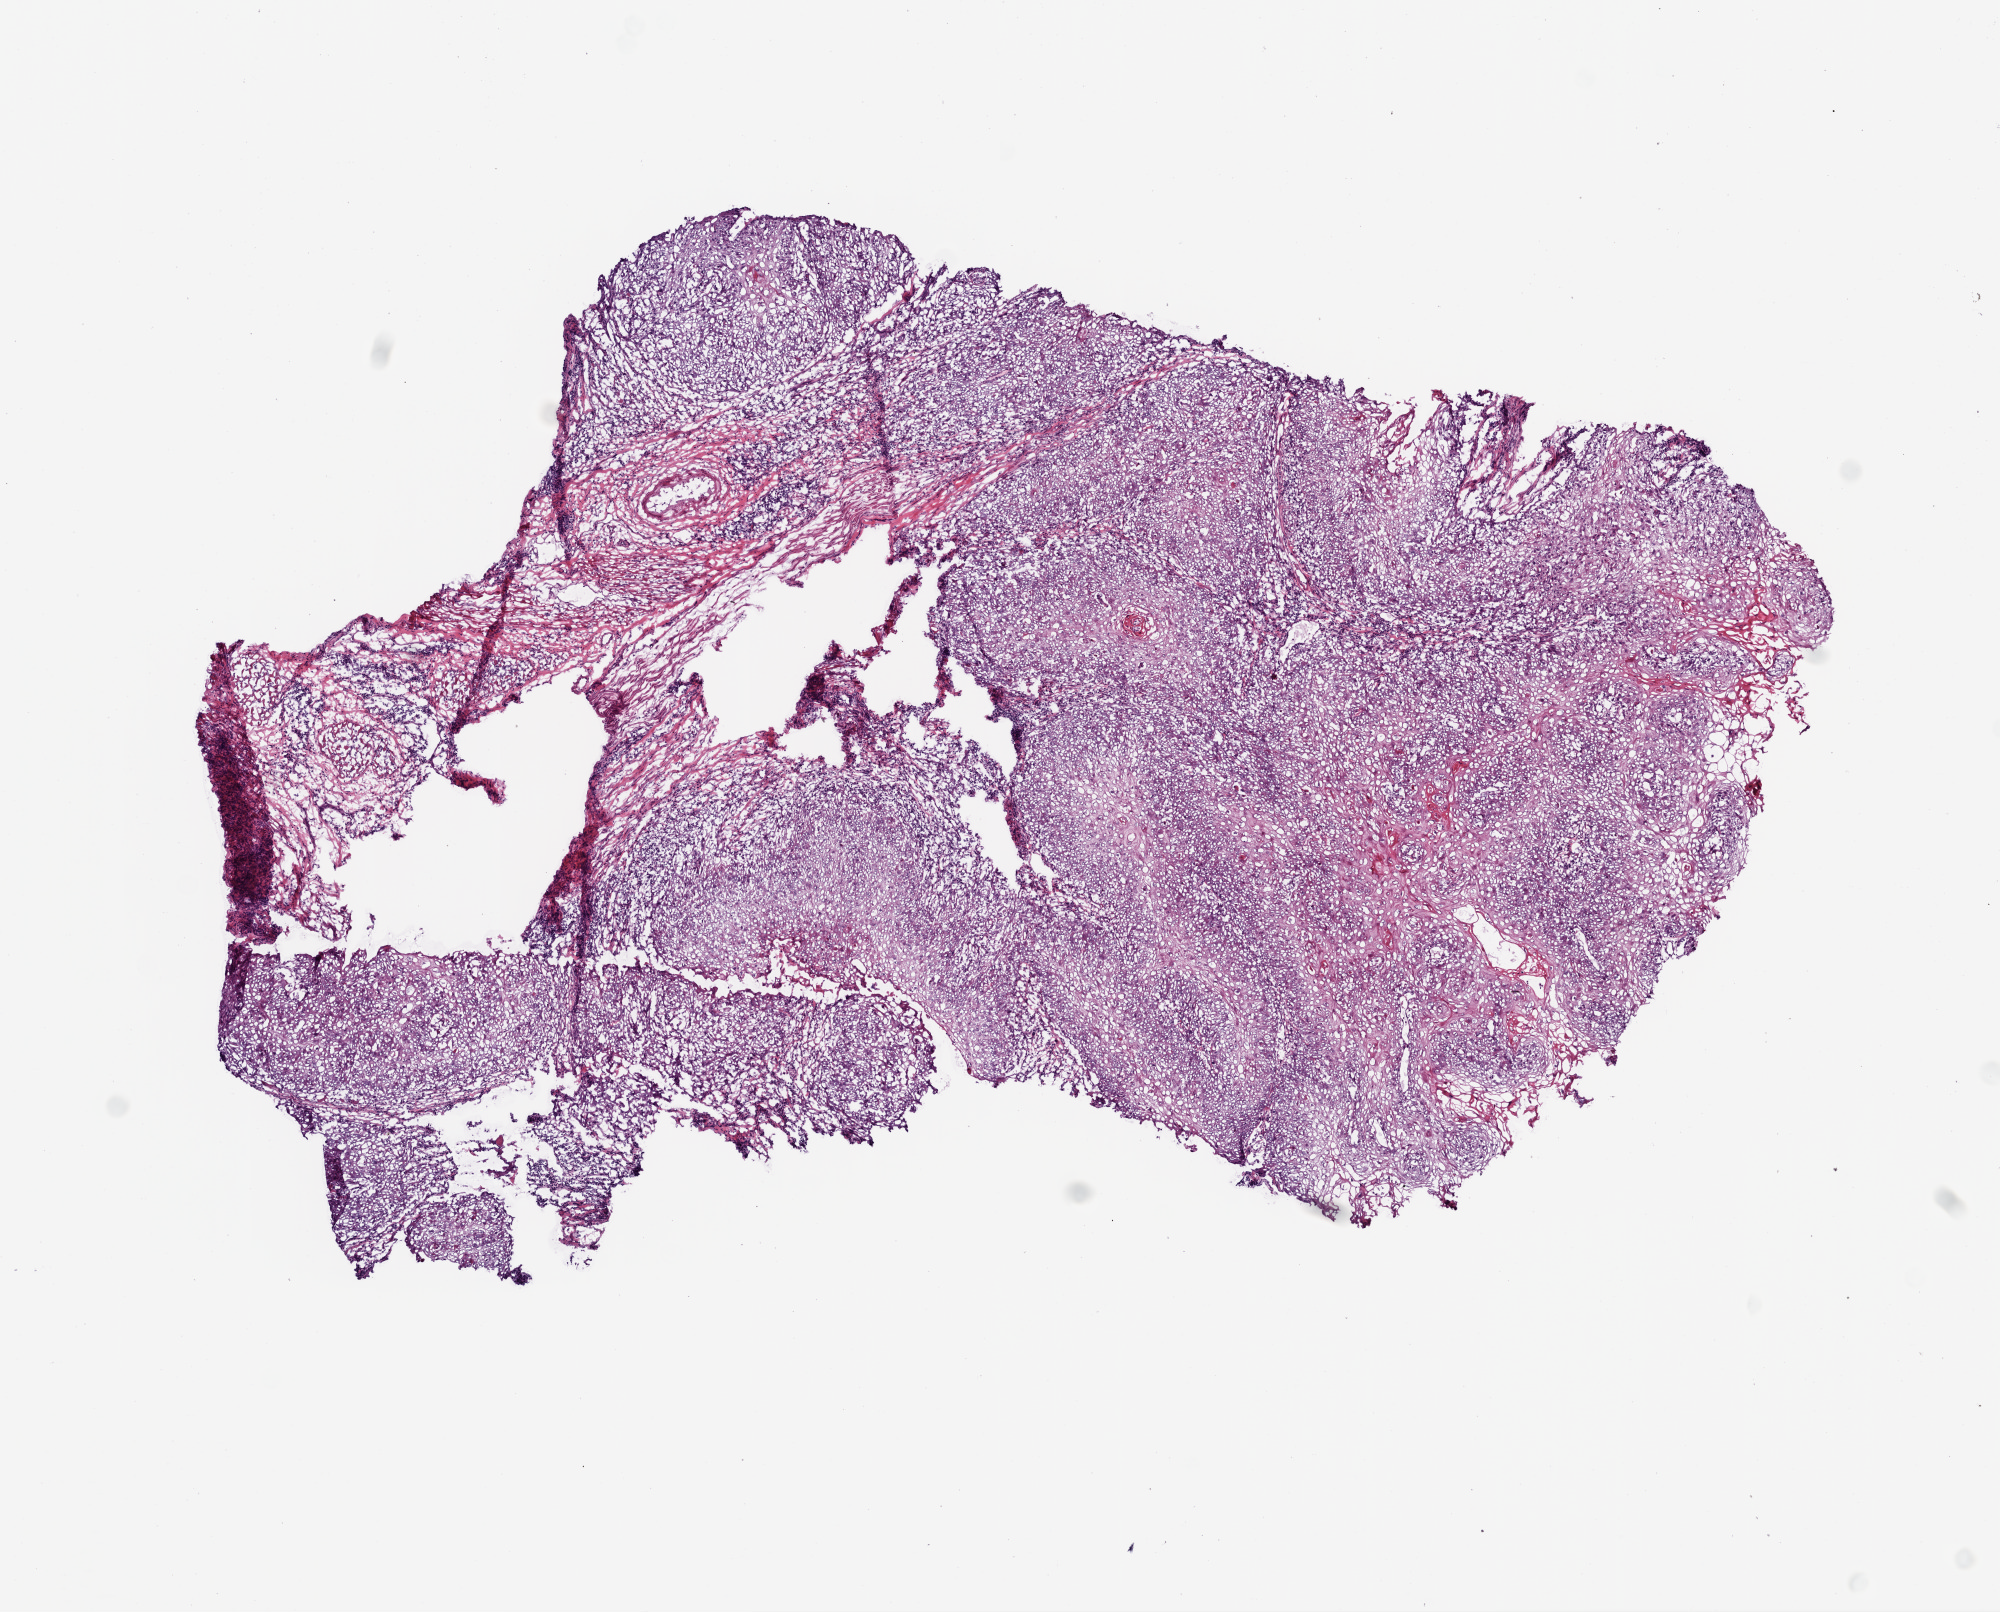
Whole-slide histology image, H&E-stained — whole scanned area (about 8.0 x 6.5 mm, acquisition: 20x scan) shown as a low-resolution overview. Frozen section from the bottom of the tissue portion. Sample: primary tumour, head and neck. Female, age 61 years at initial diagnosis.
Histologic diagnosis: Squamous cell carcinoma, NOS.